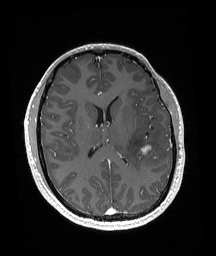
Brain MRI from a brain-tumour surgery series, one axial slice; position 78 of 192 along the scan axis; T1-weighted post-contrast; 1 mm slice thickness; 216 × 256 image matrix, field of view 211 × 250 mm. Case-level facts recorded for this patient, not image findings: histopathology: Glioneuronal tumor; WHO grade: 2.
Annotated regions visible in this slice (manually delineated by an expert):
- tumour: bounding box (x1, y1, x2, y2) in pixels: (141, 143, 152, 155)